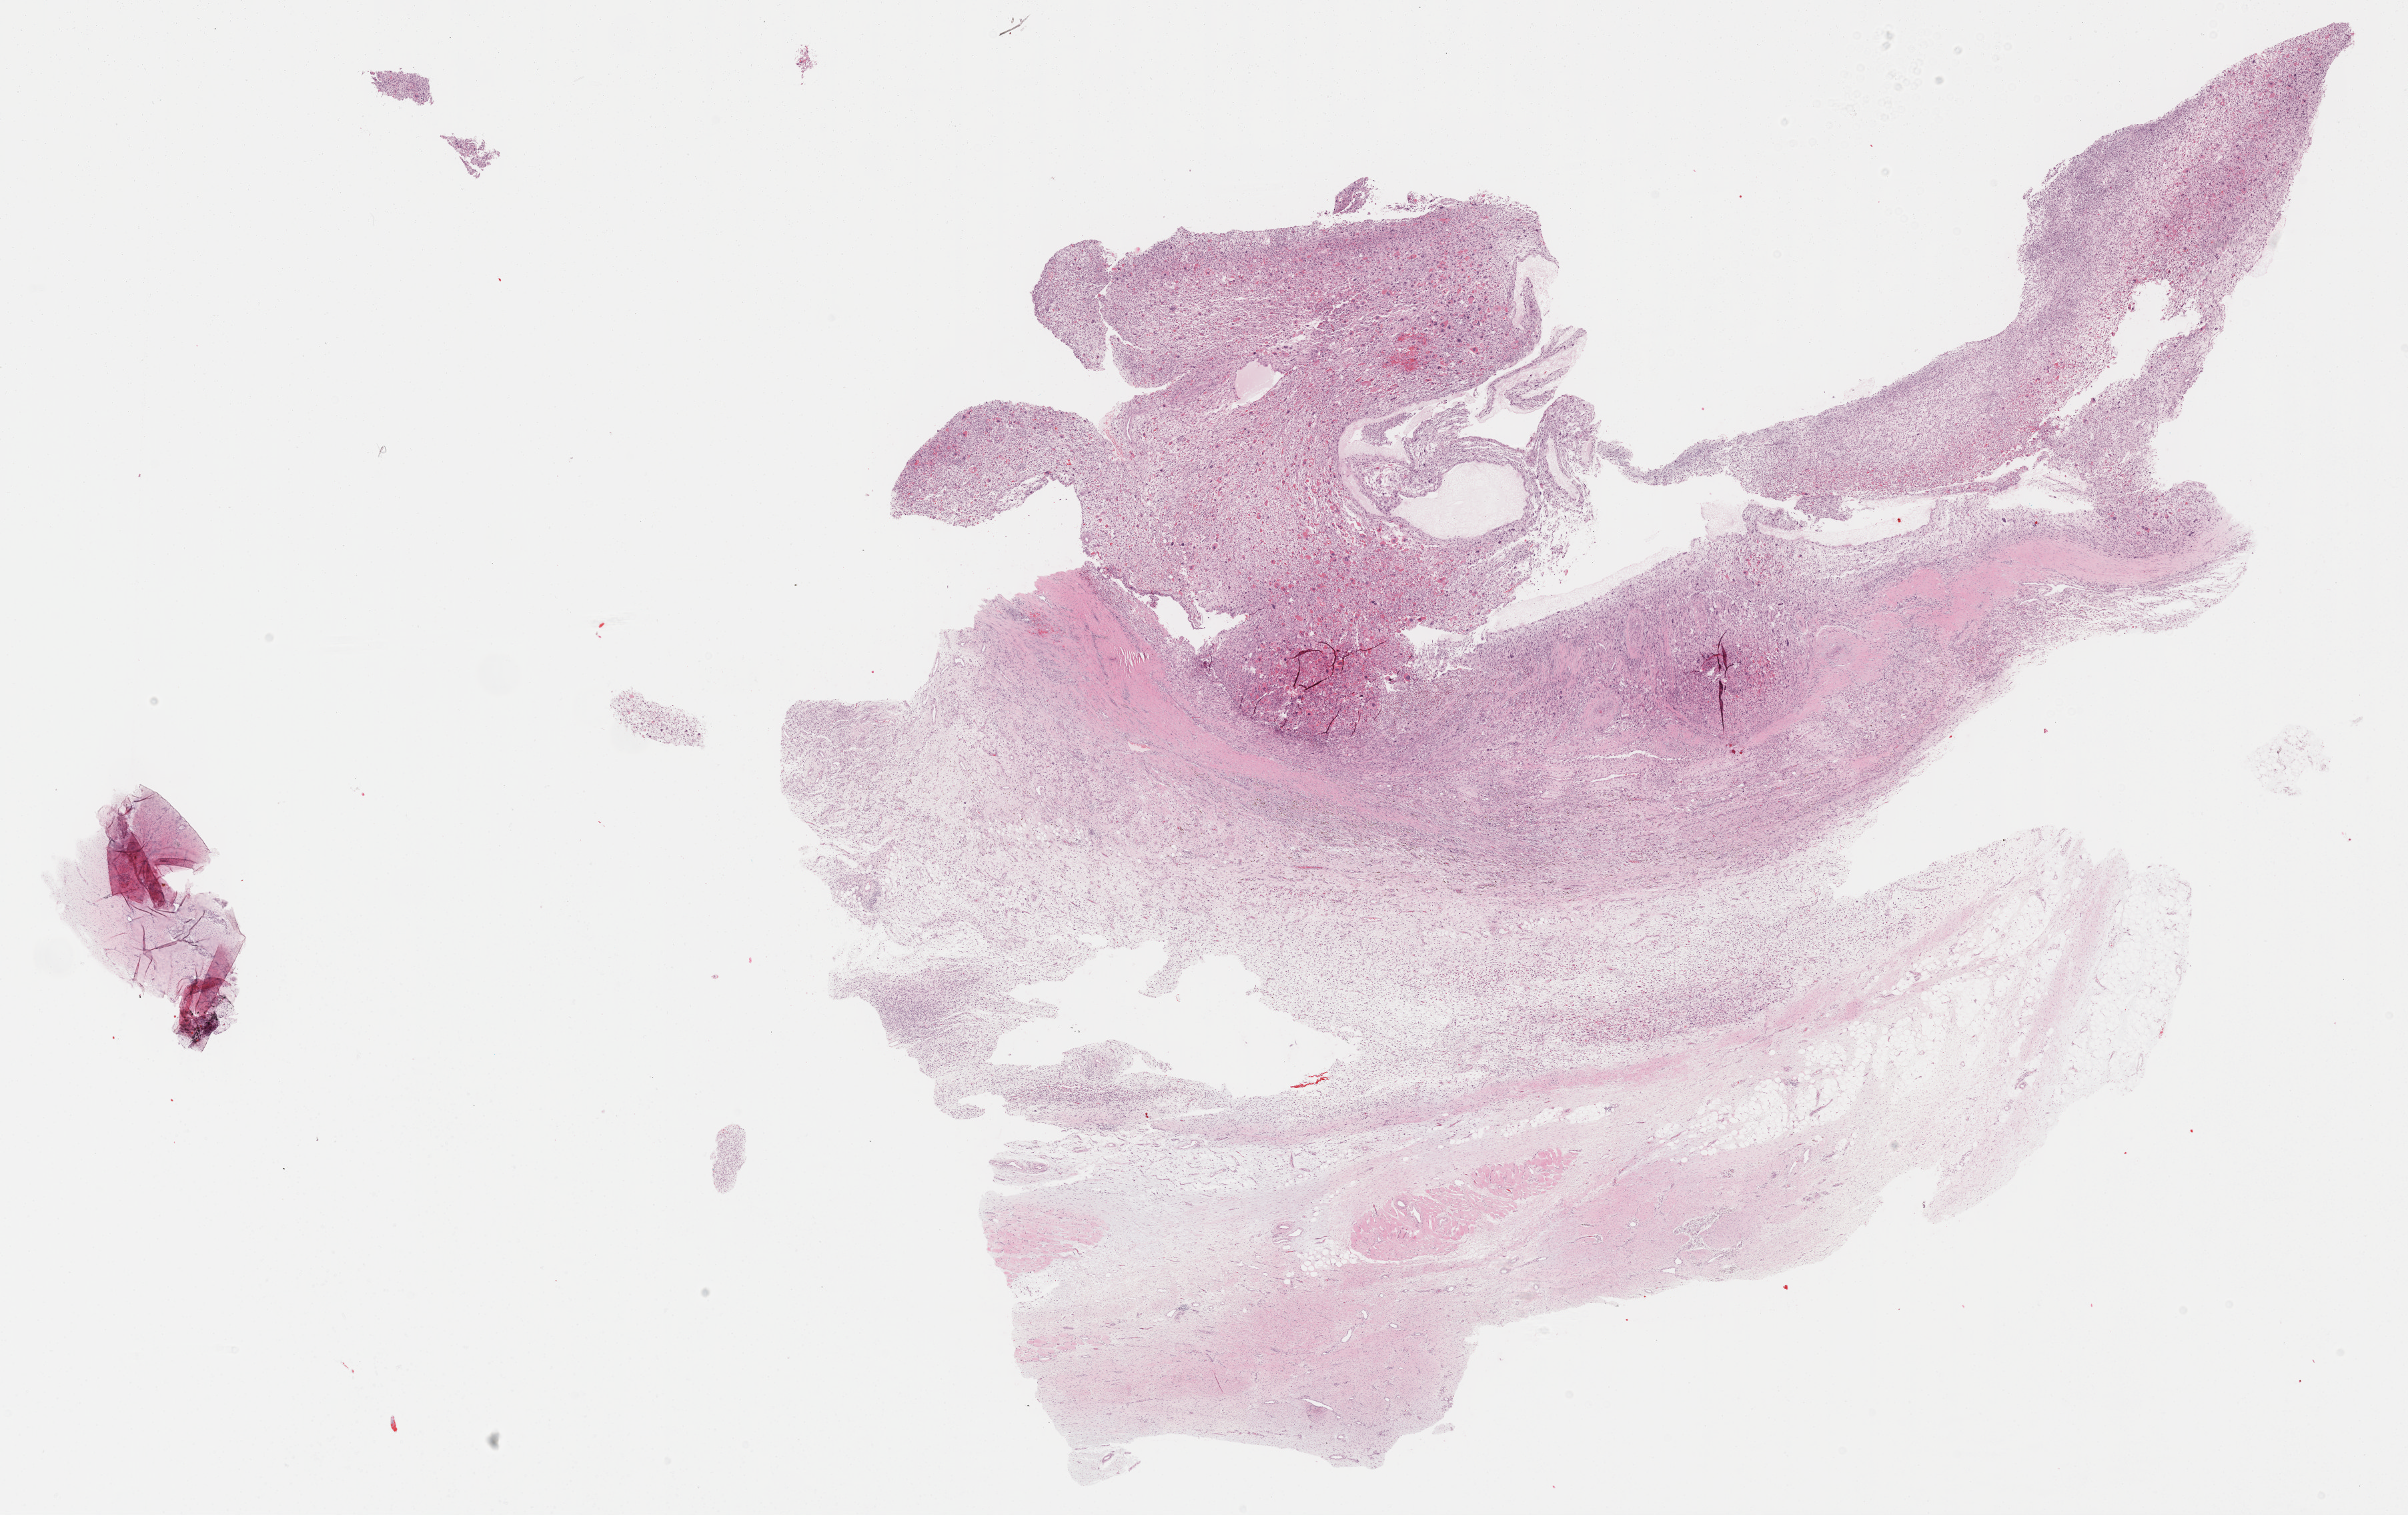
Hematoxylin and eosin (H&E) stained whole-slide image — low-resolution overview of the scanned area, about 29.2 x 18.4 mm (acquisition: 40x scan). Formalin-fixed paraffin-embedded (FFPE) diagnostic section. Connective, subcutaneous and other soft tissues, primary tumour sample. Female patient; age at initial diagnosis 54 years.
Diagnosis: Fibromyxosarcoma (connective, subcutaneous and other soft tissues of lower limb and hip).